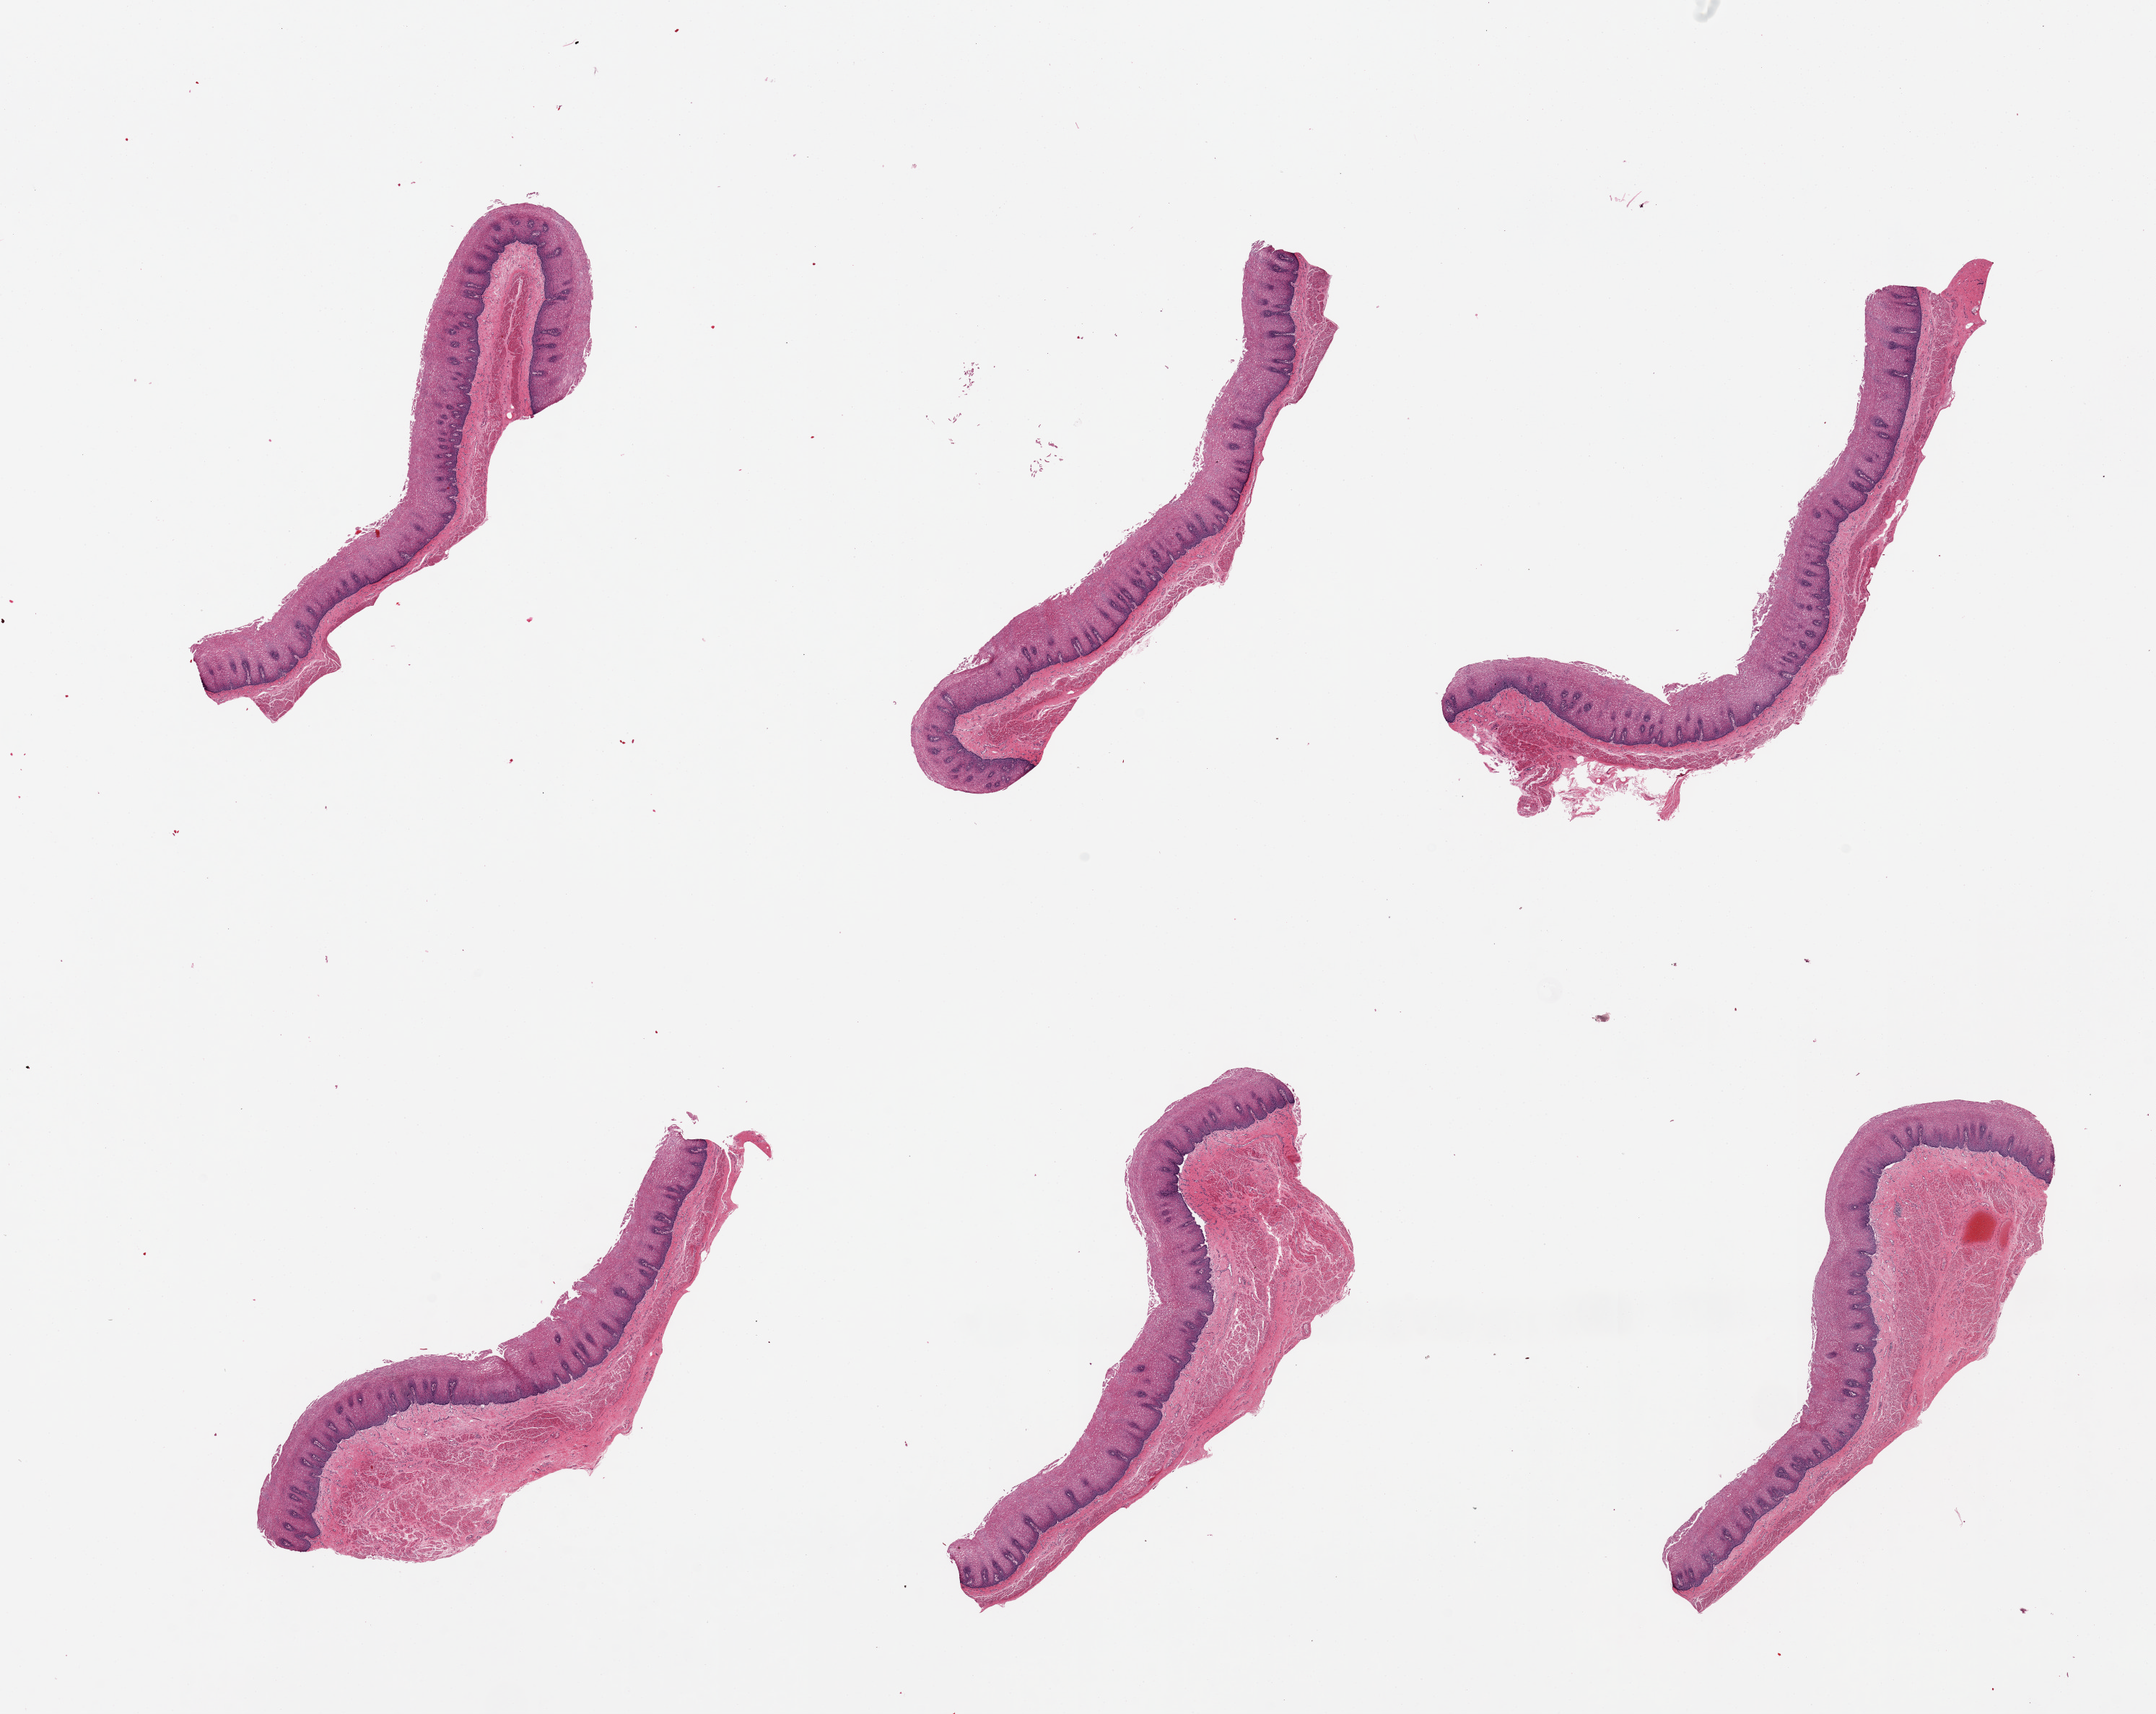
Hematoxylin and eosin (H&E) whole-slide image, brightfield — whole scanned area (about 23.6 x 18.8 mm) shown as a low-resolution overview. PAXgene-fixed paraffin-embedded (PFPE) section. Target tissue: esophageal mucous membrane. Tissue donor sample. Female donor.
Review note (as recorded): 6 pieces, squamous mucosa ~ 40-75% thickness.